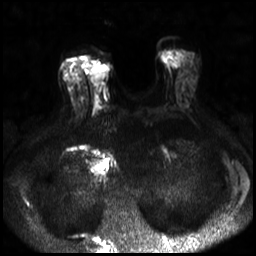
Breast MRI, one axial slice. Slice 10 of 30 in the series (ordered by position). Diffusion-weighted series; image 2 of 4 stored at this slice position (different b-values; order by instance number). 3 T. 4 mm slice thickness. 256 × 256 image matrix, field of view 320 × 320 mm. Female patient.
Annotated regions visible in this slice (expert manual segmentation):
- tumour on diffusion-weighted imaging: box from (x=91, y=65) to (x=108, y=84) px